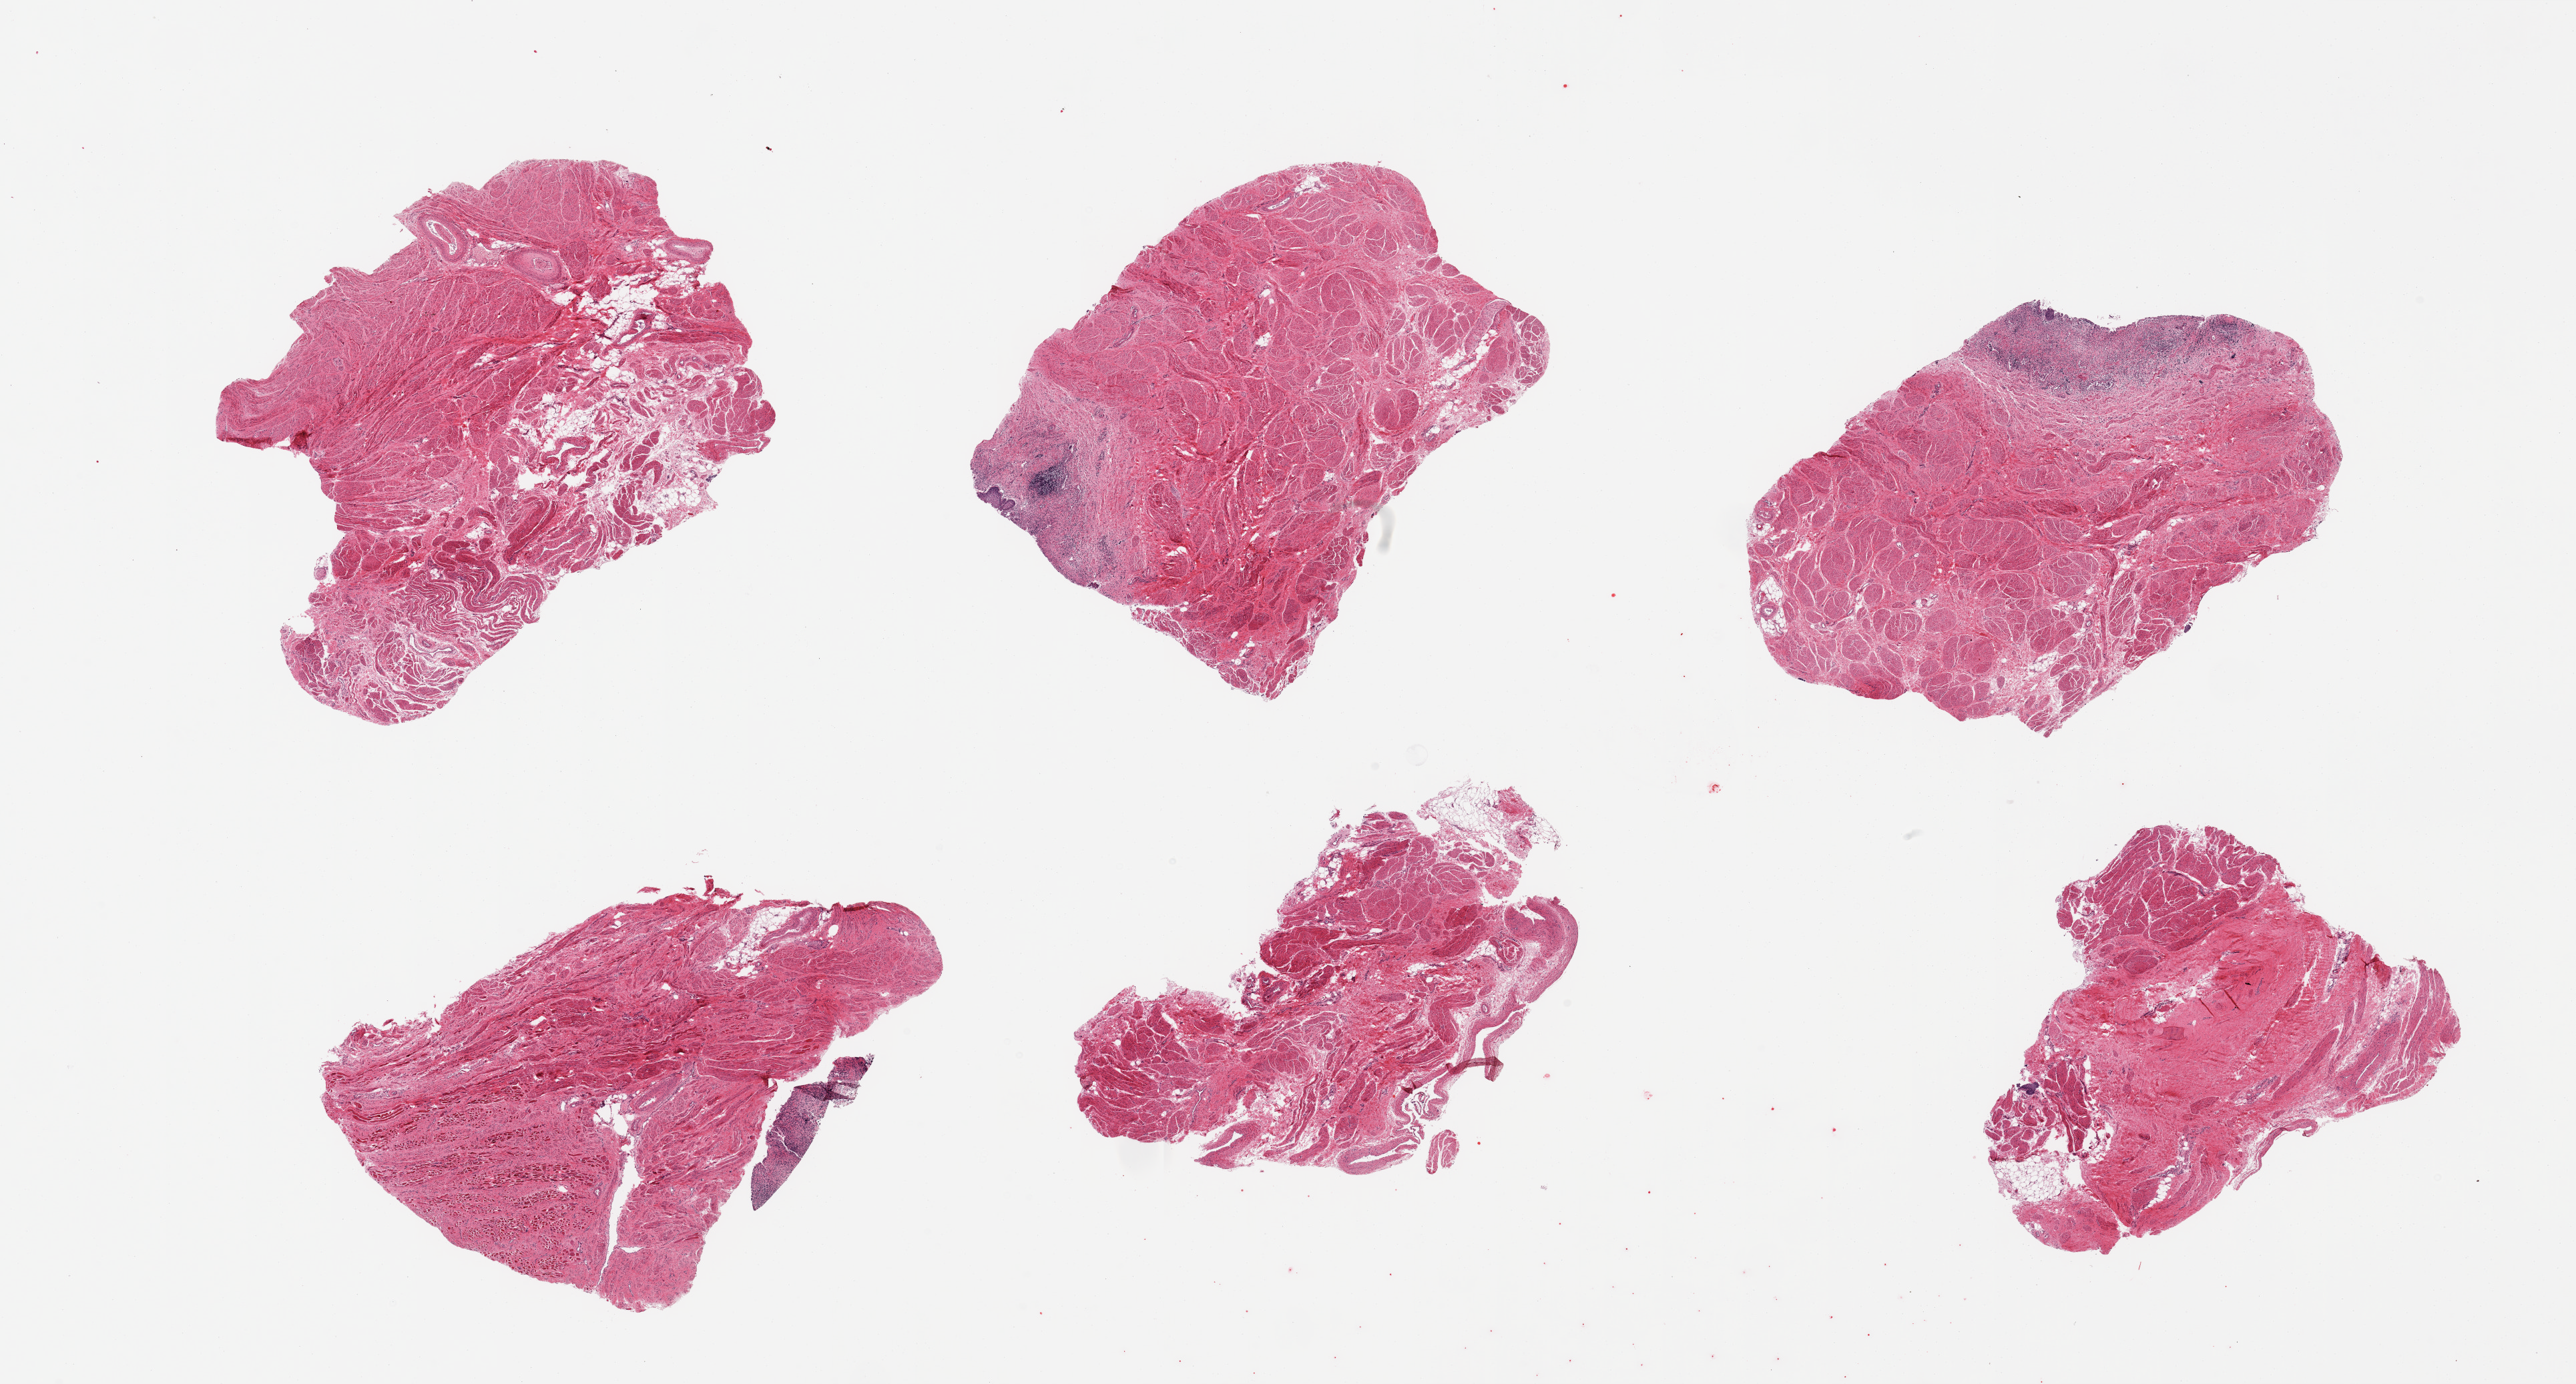
Haematoxylin and eosin whole-slide image, brightfield — low-resolution overview of the scanned area, about 30.5 x 16.4 mm; PAXgene-fixed paraffin-embedded (PFPE) section; section of vagina (target tissue); donor tissue sample. Female donor.
Reviewer comment on this tissue sample: 6 pieces; variable fragments with minimal squamous epithelium in 3, associated chronic inflammation, muscle.